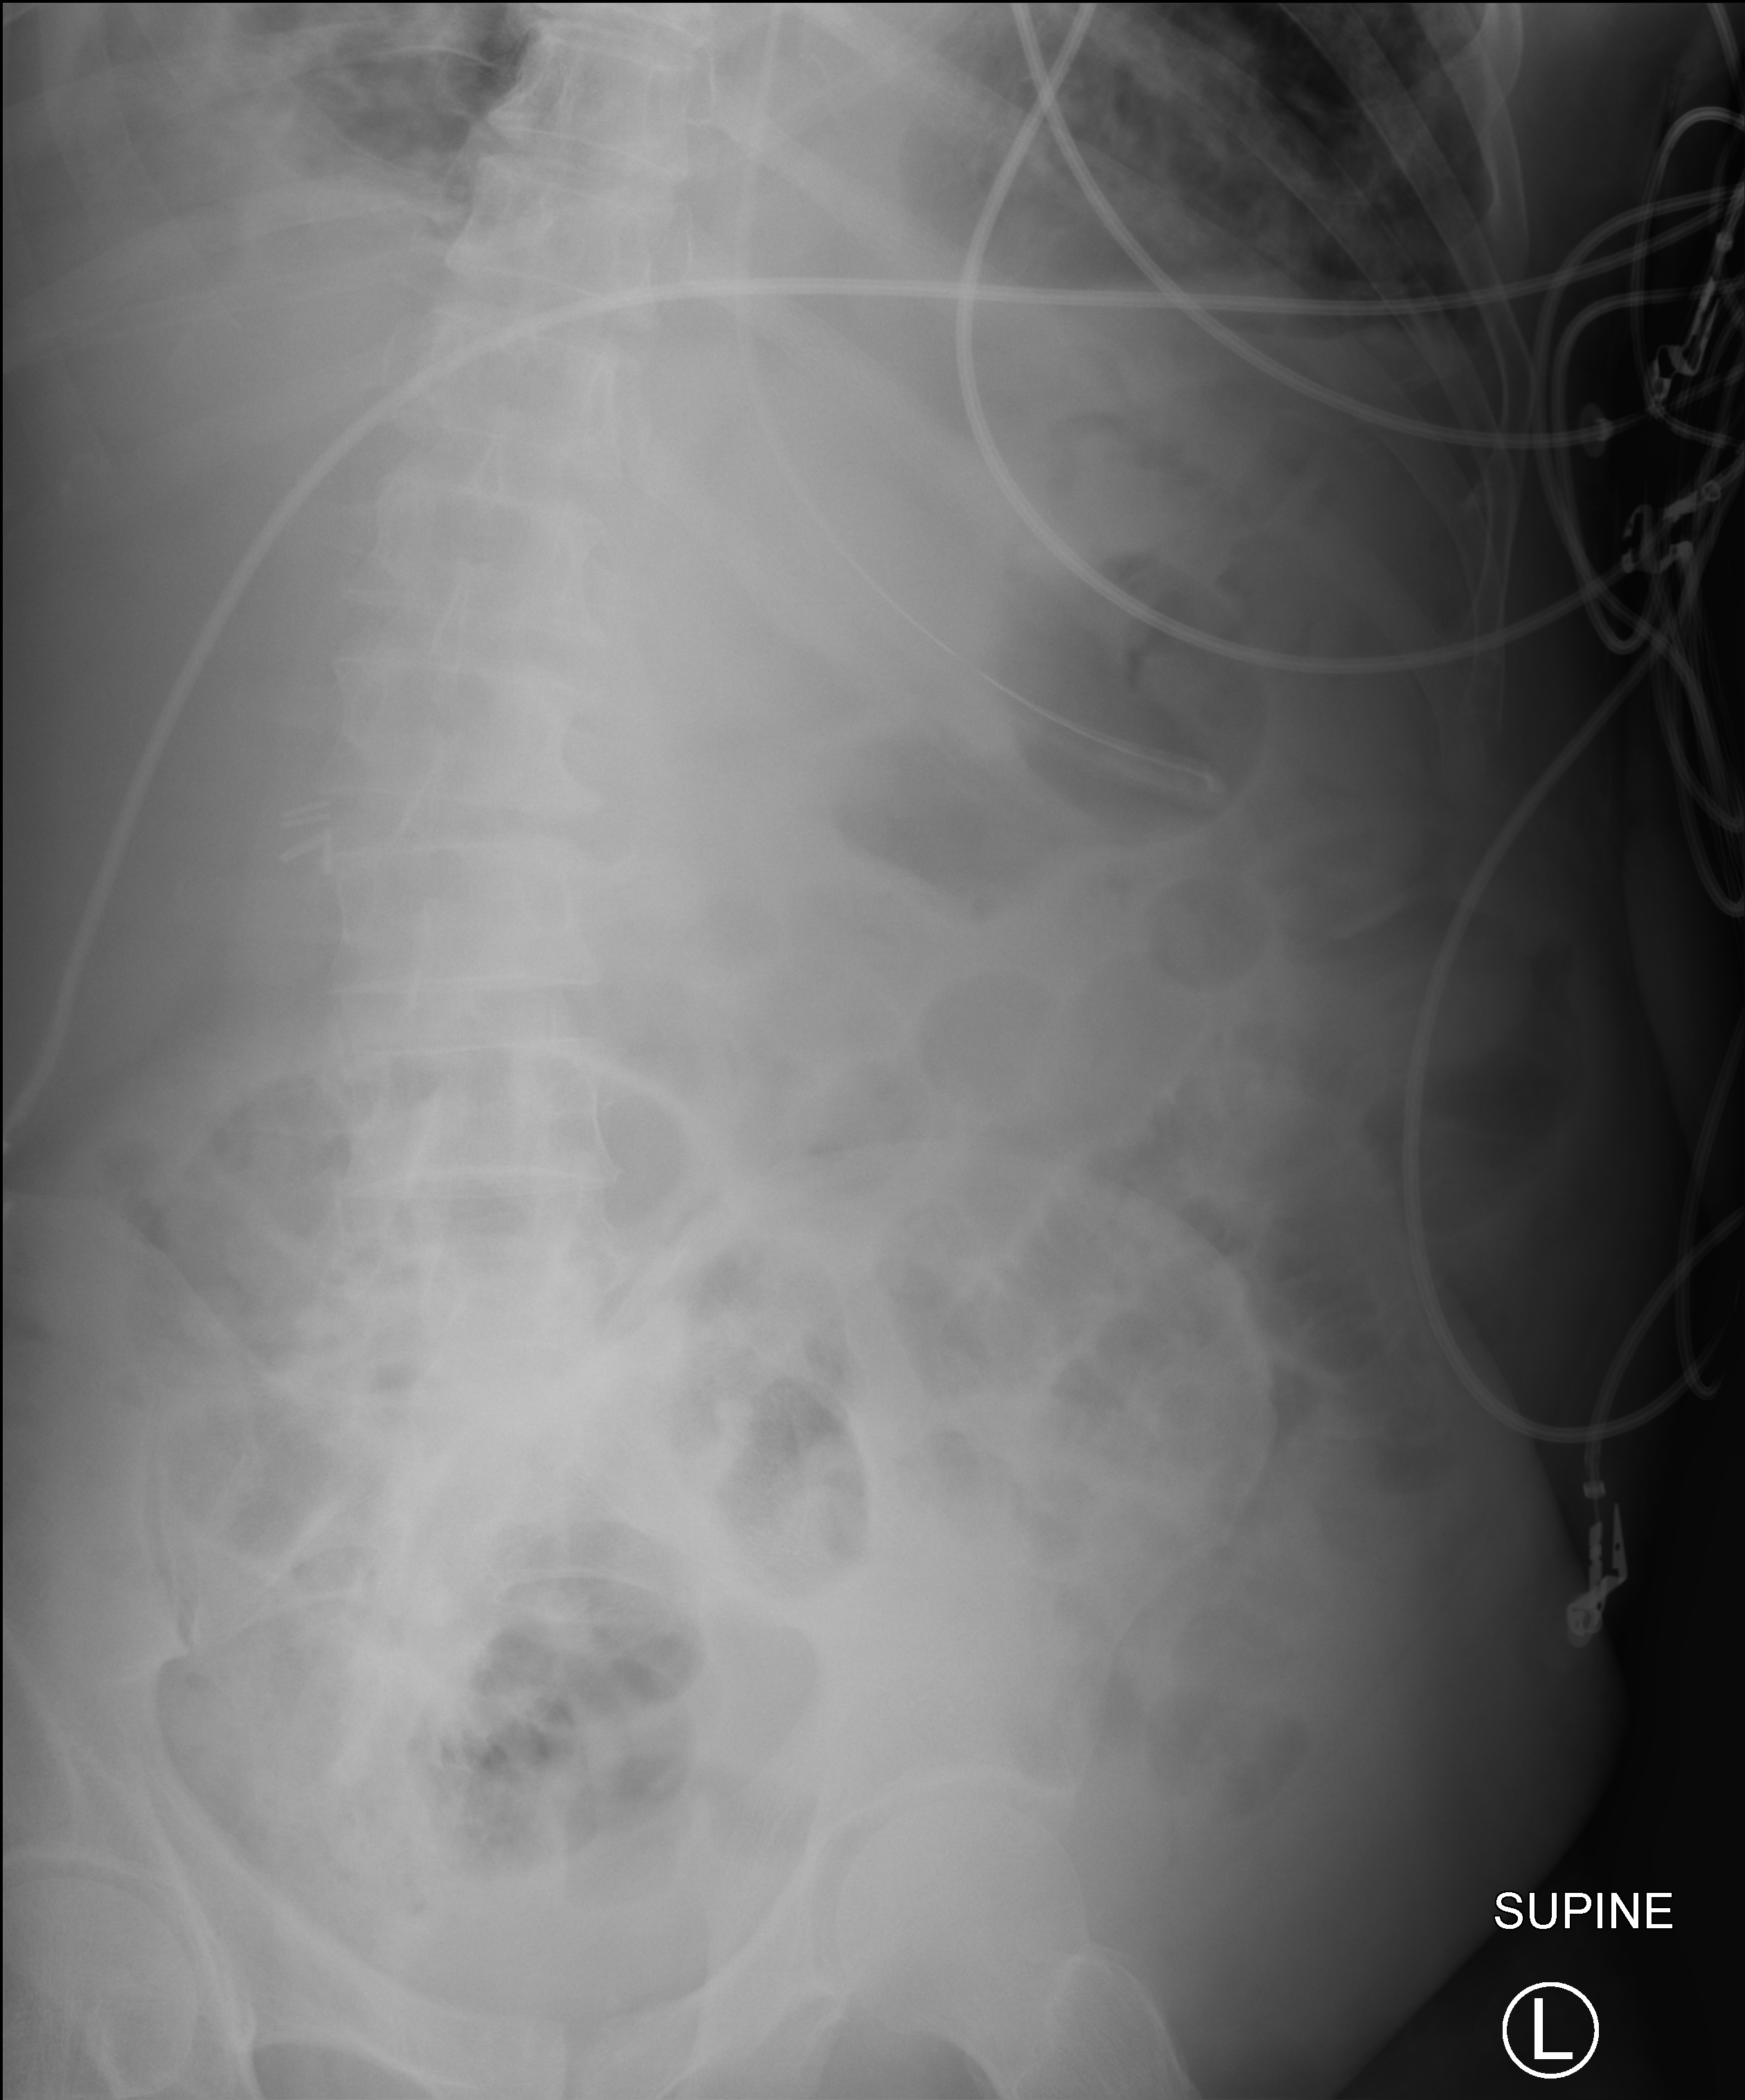
Abdomen X-ray (portable); anteroposterior (AP) projection. Patient hospitalised with COVID-19; male, aged 75–90 years.
Hospital-stay facts (about this admission, not read from this image; timing relative to this image not recorded): mechanically ventilated during this hospital stay: yes.